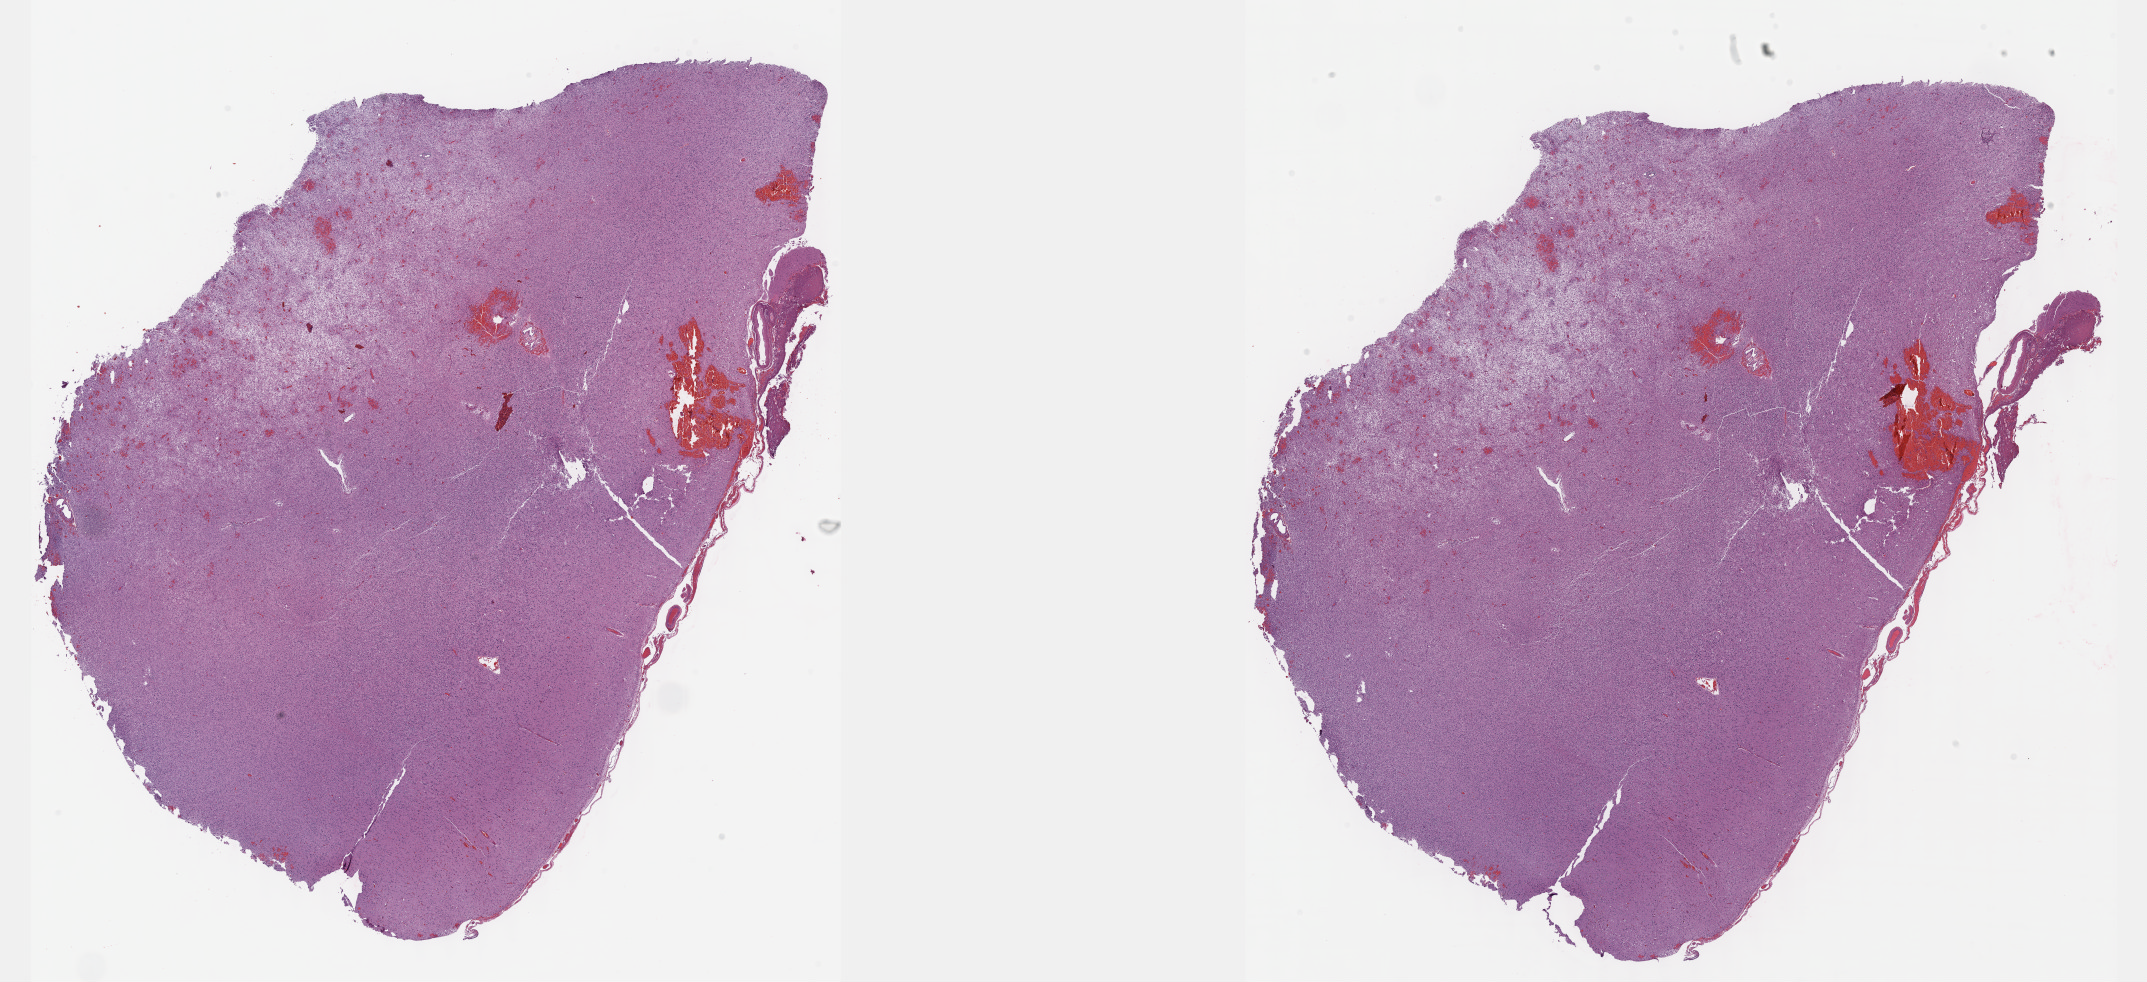
Whole-slide histology image, H&E-stained — a low-resolution overview of the entire scanned area, about 34.7 x 15.9 mm. FFPE section. Sample: primary tumour, brain. Female patient; age at initial diagnosis 52 years. Histologic grade: G3 (poorly differentiated).
Laterality: right. Diagnosis: Astrocytoma, anaplastic (cerebrum).